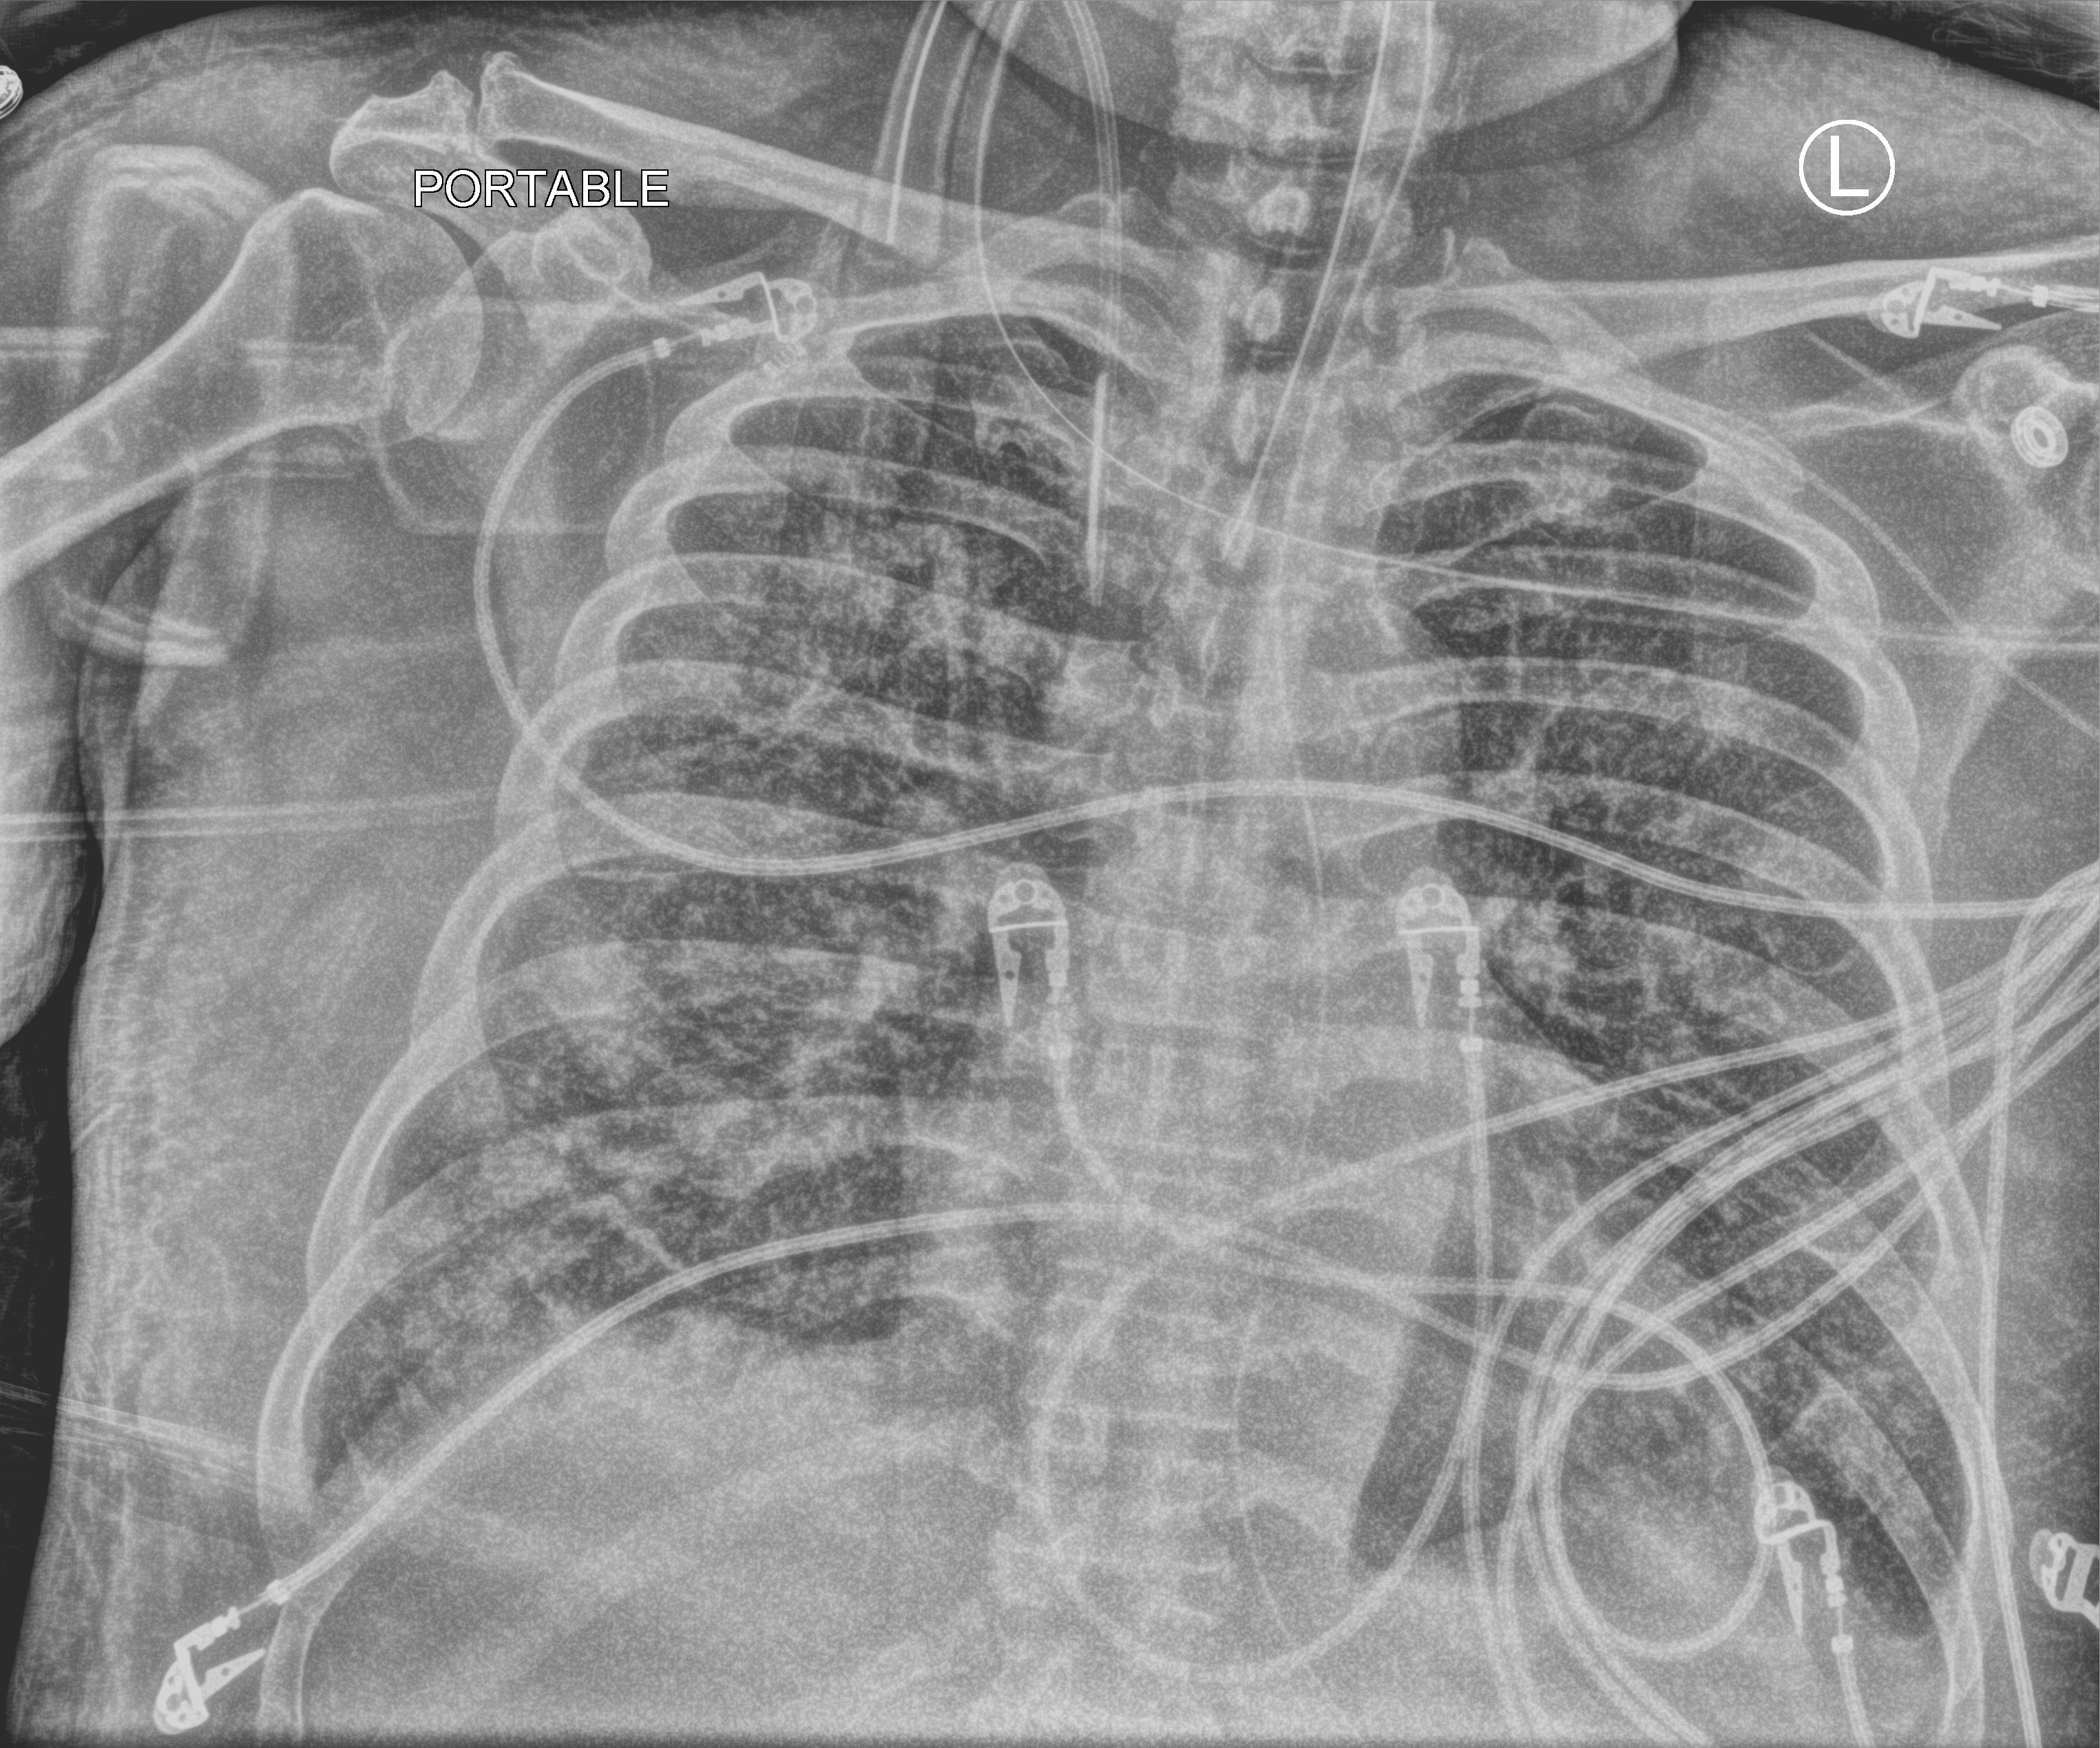
Chest X-ray (portable), anteroposterior (AP) projection. Male patient hospitalised with COVID-19, age 60–74 years.
From the hospital-stay record, not from the radiograph (when in the stay this image was taken is not recorded):
- admitted to intensive care during this hospital stay: yes